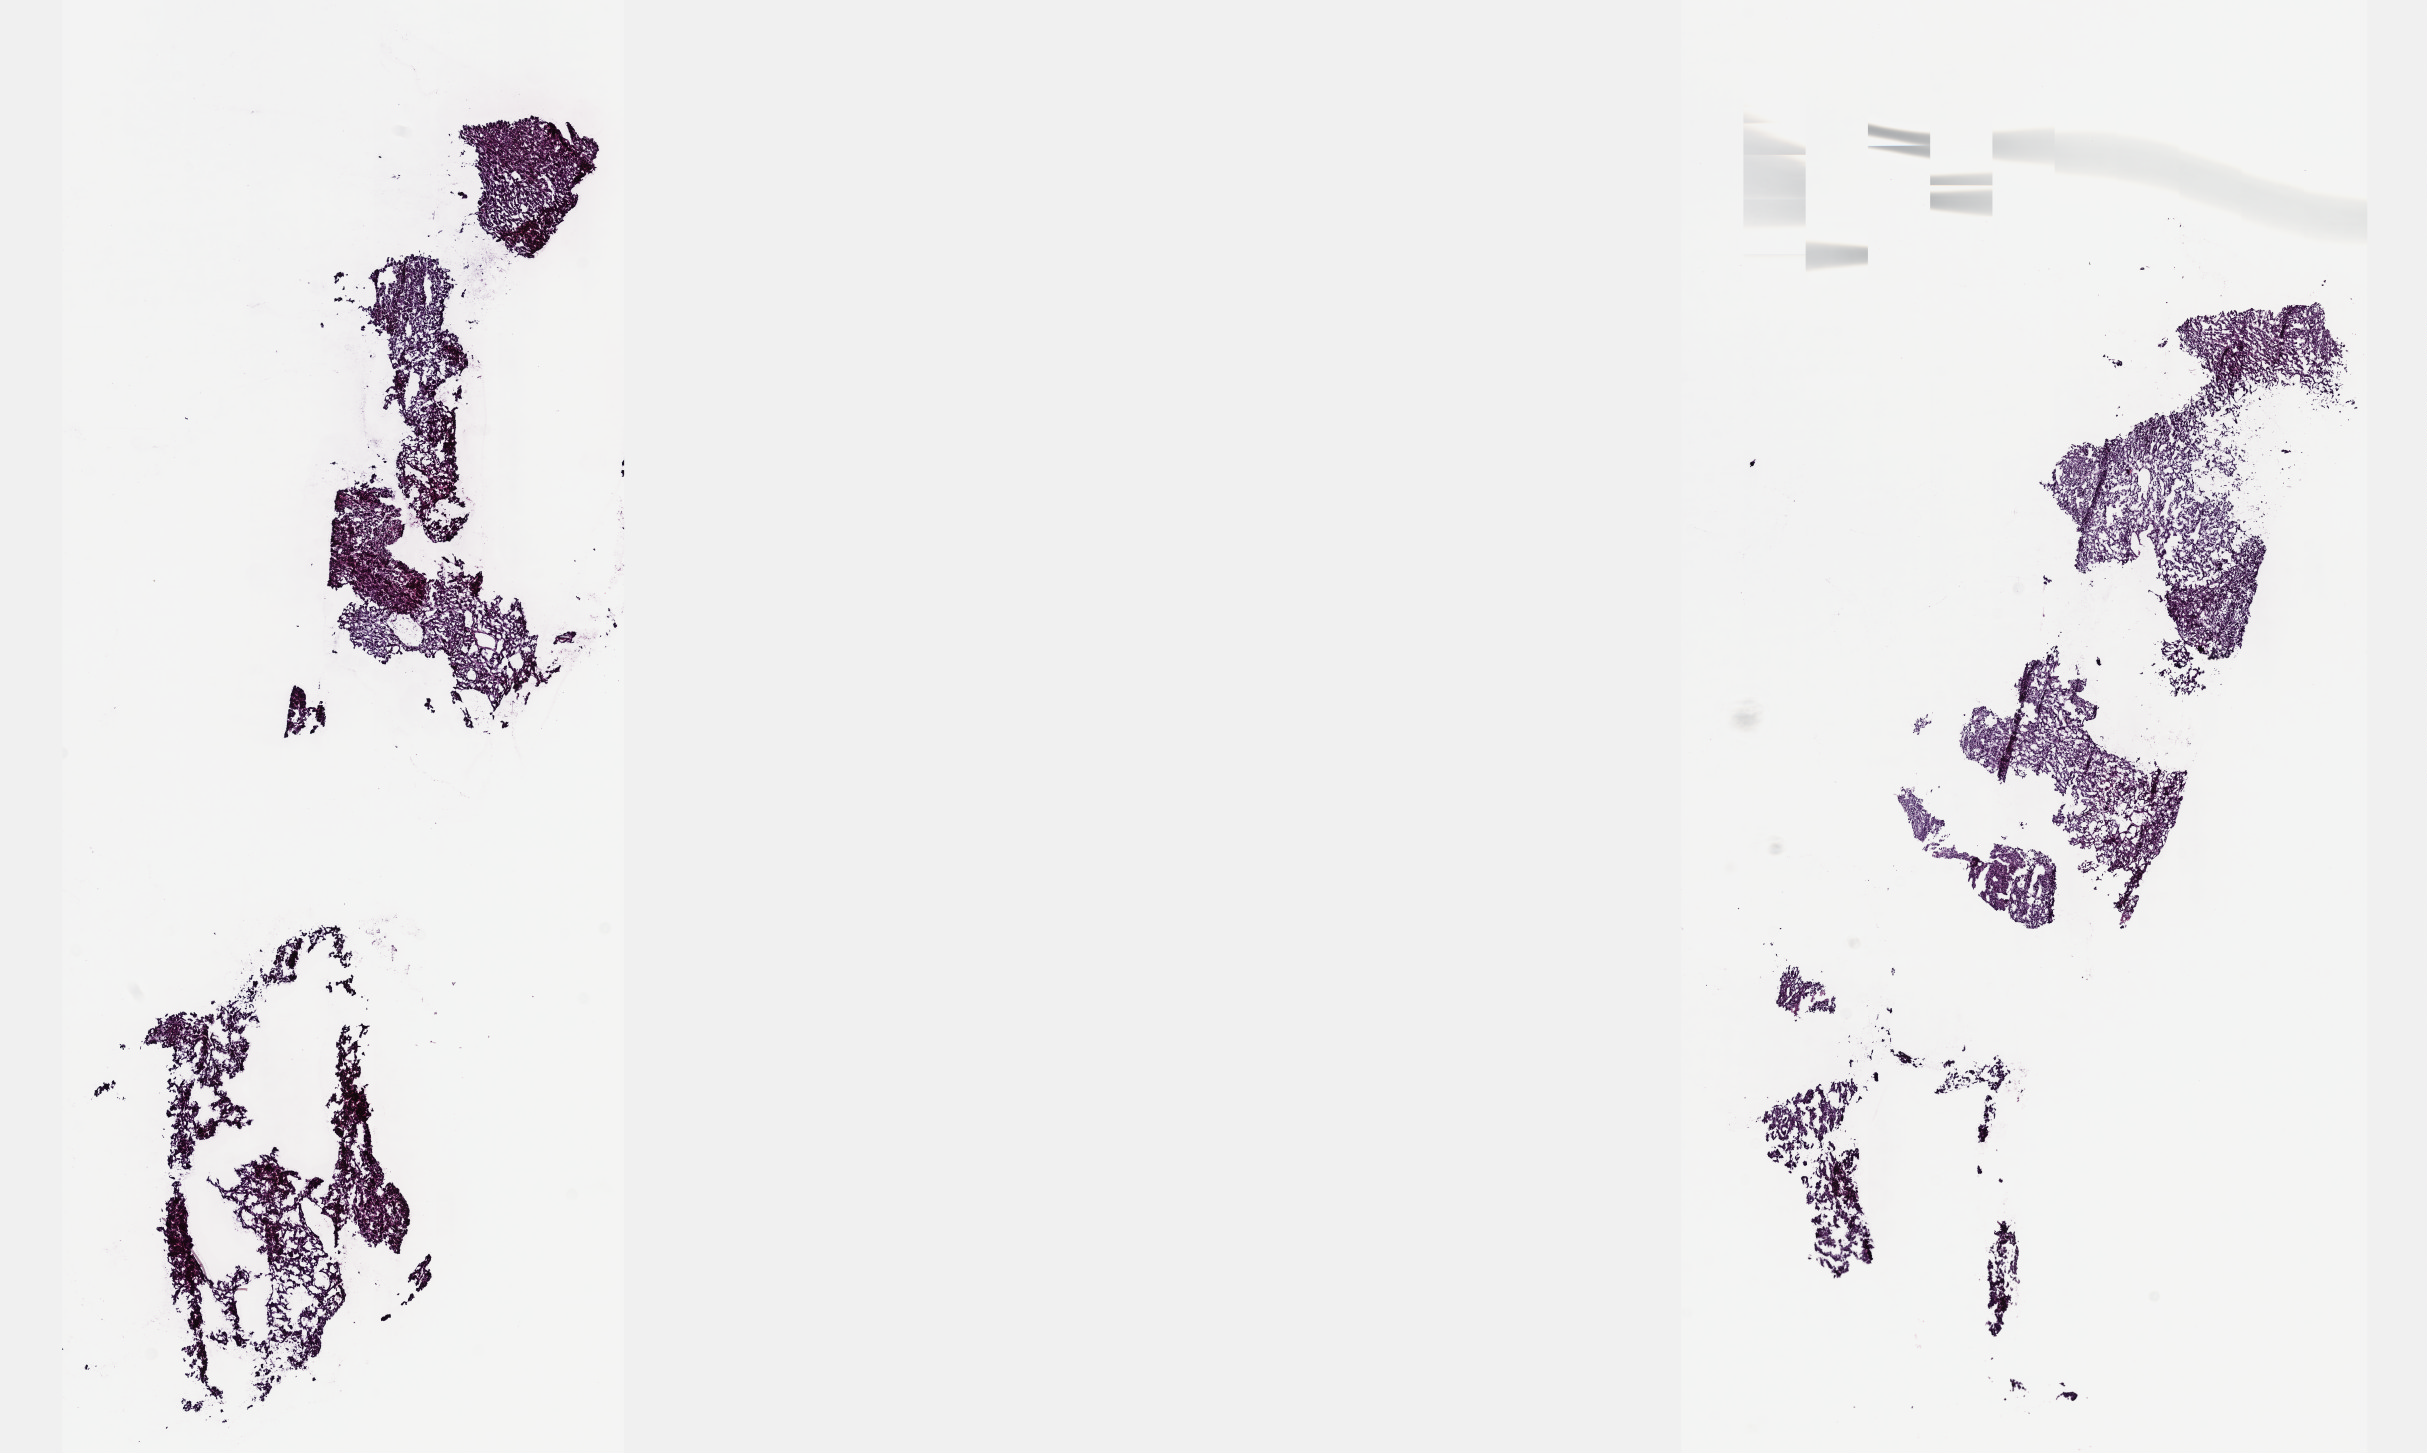
Digitized H&E-stained tissue section (whole slide) — low-resolution overview of the scanned area, about 19.6 x 11.7 mm (acquisition: 40x scan); frozen section from the top of the tissue portion; sample: primary tumour, liver. Male, age 69 years at initial diagnosis. Histologic grade: G2 (moderately differentiated). Slide review estimates, as recorded: tumour cells 80%, tumour nuclei 80%, normal cells 0%, stromal cells 20%, necrosis 0%. Infiltration values recorded for this section: lymphocyte infiltration 2%, monocyte infiltration 1%, neutrophil infiltration 2%.
- AJCC pathologic stage: I
- diagnosis: Hepatocellular carcinoma, NOS